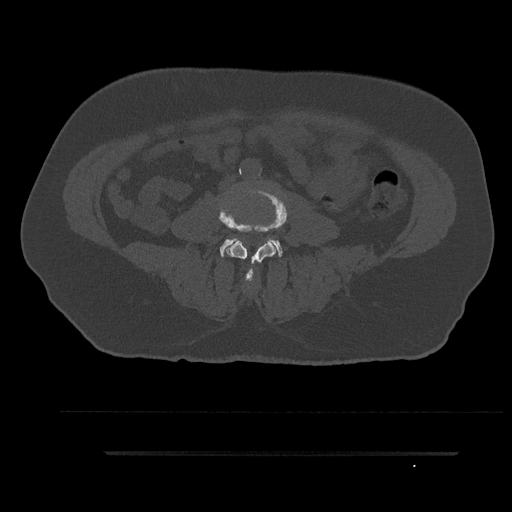
CT including the spine, one axial slice. Position 13 of 797 along the scan axis. 120 kVp. Bone window (W 1800 / L 400 HU). 512 × 512 image matrix. Male patient, age 63 years. Case-level facts recorded for this patient, not image findings: primary cancer: renal; vertebrae with lytic lesions (as recorded): T8.
Annotated regions visible in this slice (semi-automatic segmentation, software-assisted and operator-edited):
- L3 vertebra: bounding box (x1, y1, x2, y2) in pixels: (218, 188, 288, 285)
- L4 vertebra: (219, 236, 283, 280)